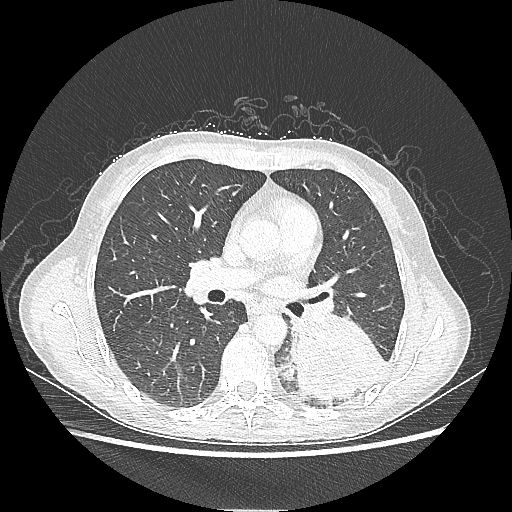
Chest CT, one axial slice. Reconstruction kernel LUNG. 80 kVp. Lung window (W 1500 / L -600 HU). 1.25 mm slice thickness. 512 × 512 image matrix, field of view 360 × 360 mm. Patient: female, 53 years. Case-level facts recorded for this patient, not image findings: clinical TNM (as recorded): T3 N0 M0.
Outlined on this slice (bounding box drawn by a radiologist):
- lung tumour (recorded histology: adenocarcinoma): bounding box [x1, y1, x2, y2] px = [287, 314, 390, 401]